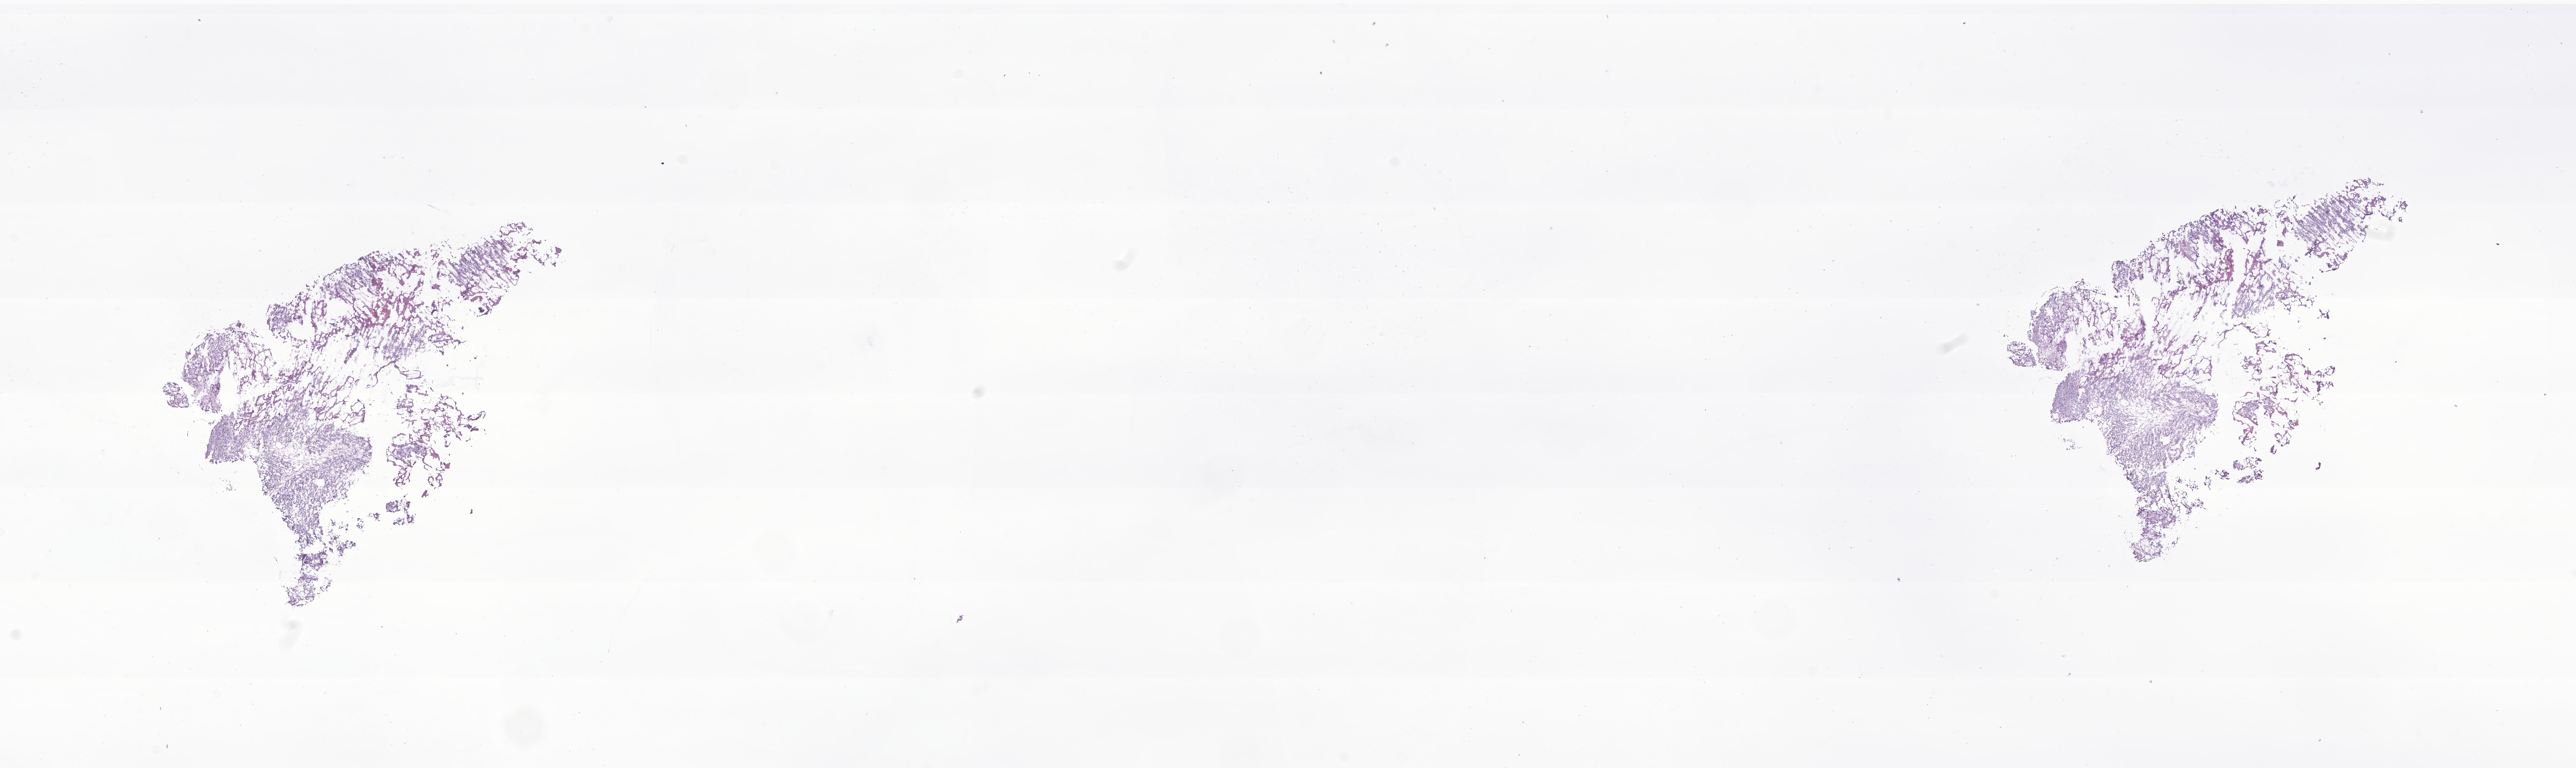
Haematoxylin and eosin whole-slide image of tumor tissue from the brain — whole scanned area (about 29.0 x 8.7 mm) shown as a low-resolution overview. Frozen section (OCT-embedded). Patient female; age 305 days.
* diagnosis: Astrocytoma, NOS